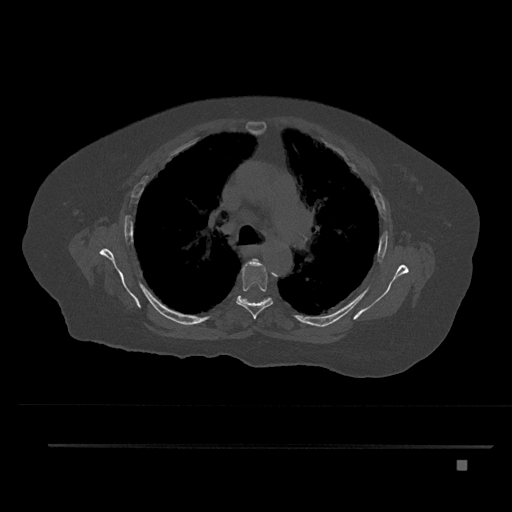
CT including the spine, one axial slice. Position 565 of 797 along the scan axis. Reconstruction kernel Br40s/3. Bone window (W 1800 / L 400 HU). 0.5 mm slice thickness. 512 × 512 image matrix. Female patient, age 76 years. From the clinical record (not read from this slice): primary cancer: lung; vertebrae with lytic lesions (as recorded): T11, L3.
Structures marked on this image (semi-automatic segmentation, software-assisted and operator-edited):
- T4 vertebra: bounding box <253,259,259,262> (left, top, right, bottom; pixels)
- T5 vertebra: <236,259,273,320>
- T6 vertebra: <236,296,270,303>